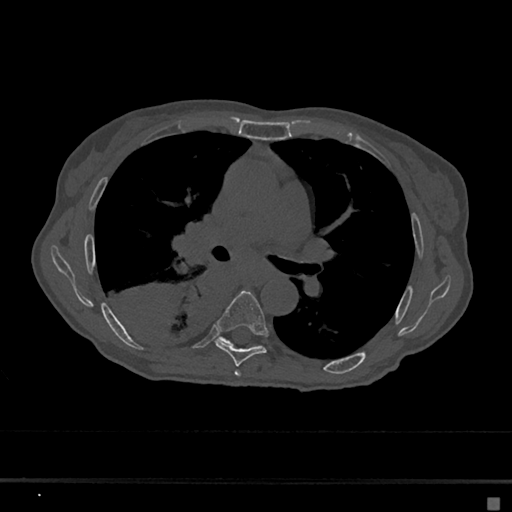
CT including the spine, one axial slice; slice 410 of 797 in the series (ordered by position); 120 kVp; bone window (W 1800 / L 400 HU); 512 × 512 image matrix. Female patient, age 68 years. From the clinical record (not read from this slice): primary cancer: renal.
Annotated regions visible in this slice (semi-automatic segmentation, software-assisted and operator-edited):
- T5 vertebra: box from (x=235, y=370) to (x=241, y=377) px
- T6 vertebra: (x=214, y=291)–(x=267, y=367)
- T7 vertebra: (x=220, y=337)–(x=257, y=347)